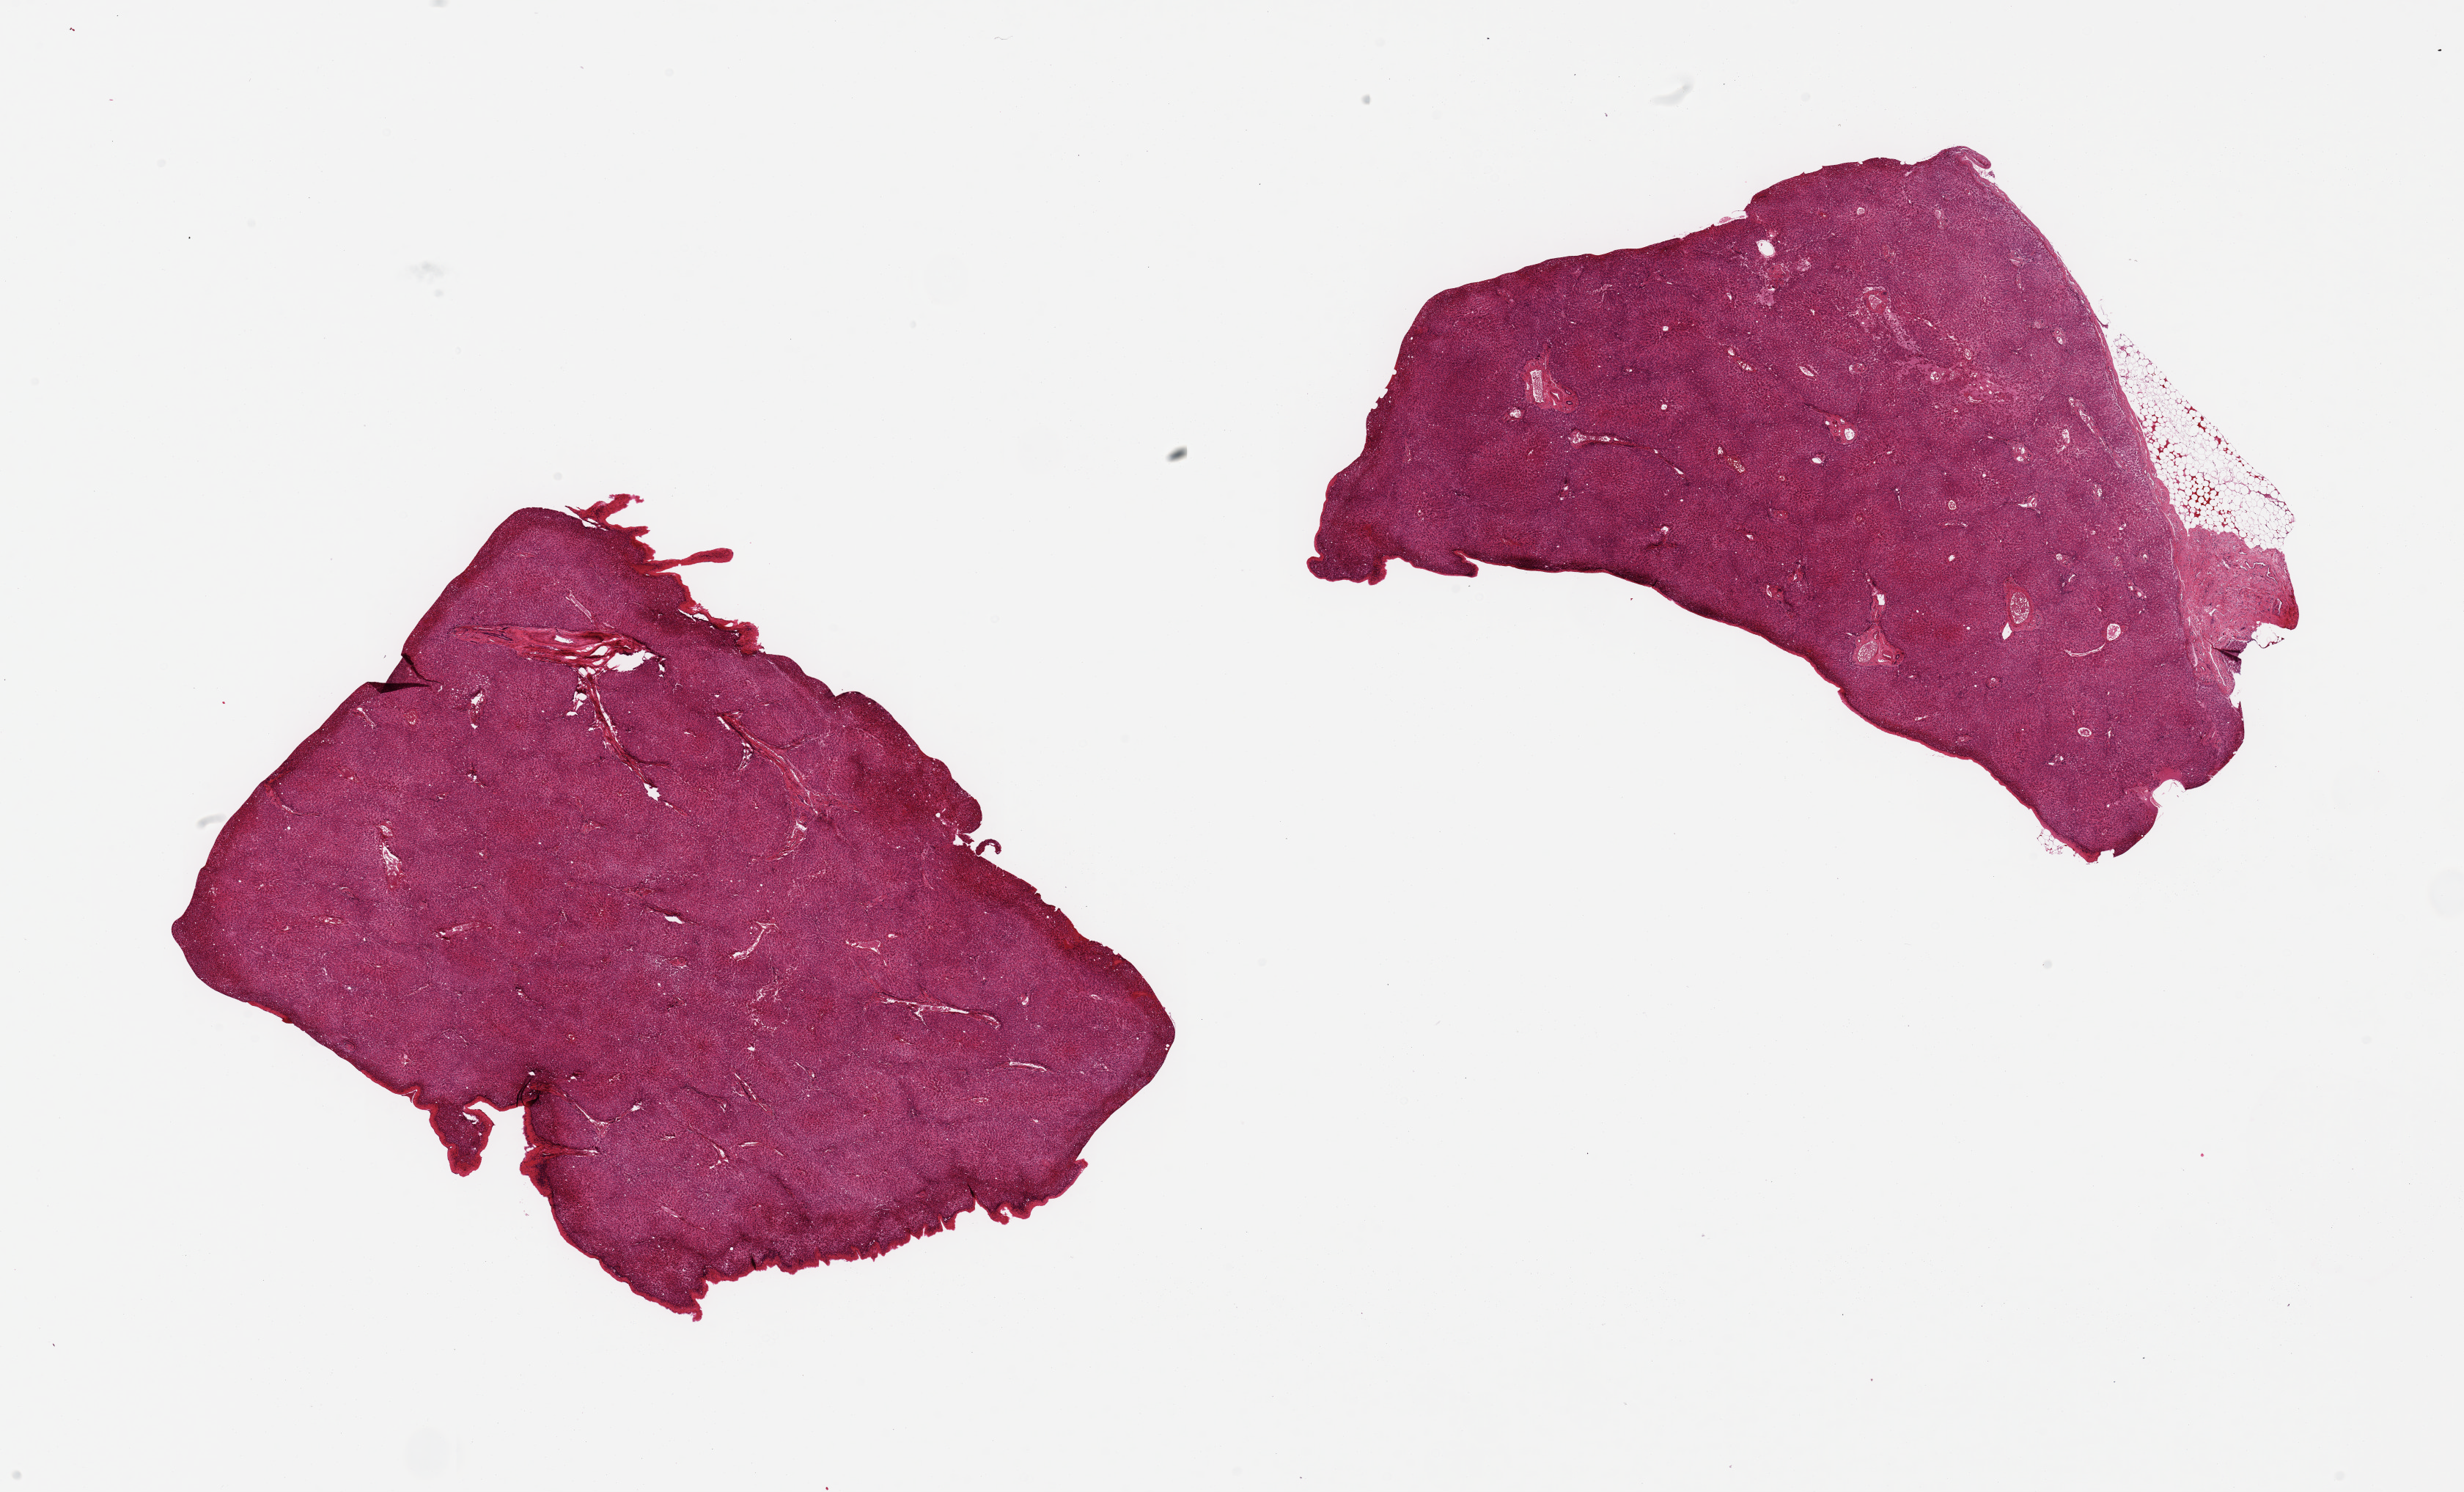
Digitized H&E-stained section, low-resolution overview of the scanned area, about 26.6 x 16.1 mm (from a 20x scan). PAXgene-fixed, paraffin-embedded tissue. Section of liver (target tissue). Tissue donor sample.
• reviewer comment on this tissue sample: 2 pieces, mild microvesicular steatosis